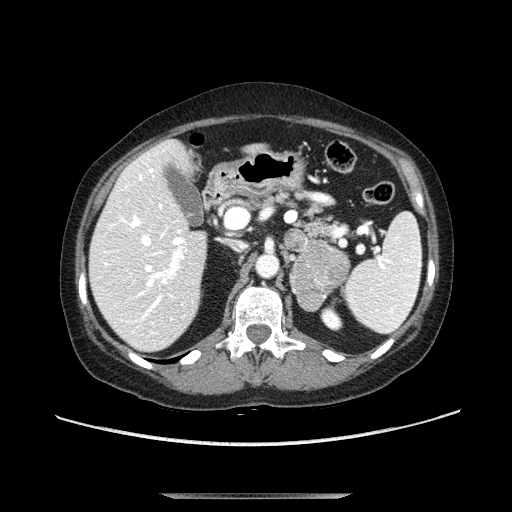
Contrast-enhanced abdominal CT, one axial slice; position 64 of 107 along the scan axis; soft-tissue window (W 400 / L 40 HU); 512 × 512 image matrix. Female patient. Case-level facts recorded for this patient, not image findings: diagnosis: adrenocortical carcinoma; tumour side: left adrenal; tumour size at pathology: 7.5 cm; Ki-67 index: 9 %; stage (as recorded): 3.
Annotated regions visible in this slice (semi-automatic segmentation, software-assisted and operator-edited):
- mass: bounding box (x1, y1, x2, y2) in pixels: (290, 242, 351, 311)